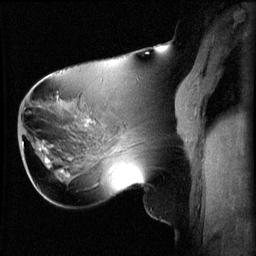
Breast MRI (dynamic contrast-enhanced), one sagittal slice; slice 29 of 60 in the series (ordered by position); 3 images stored at this slice position (order not interpretable as contrast timing); 1.5 T; TE 4.2 ms, TR 8.2 ms; 256 × 256 image matrix. Female patient, age 62 years.
Structures marked on this image (semi-automatically segmented with operator editing):
- analysis volume of interest (the breast-tissue region the enhancement analysis was run in; not a lesion): bounding box [x1, y1, x2, y2] px = [26, 126, 59, 165]
- tumour enhancement mask (voxels above the 70 % enhancement threshold inside the analysis volume of interest): [40, 150, 51, 163]